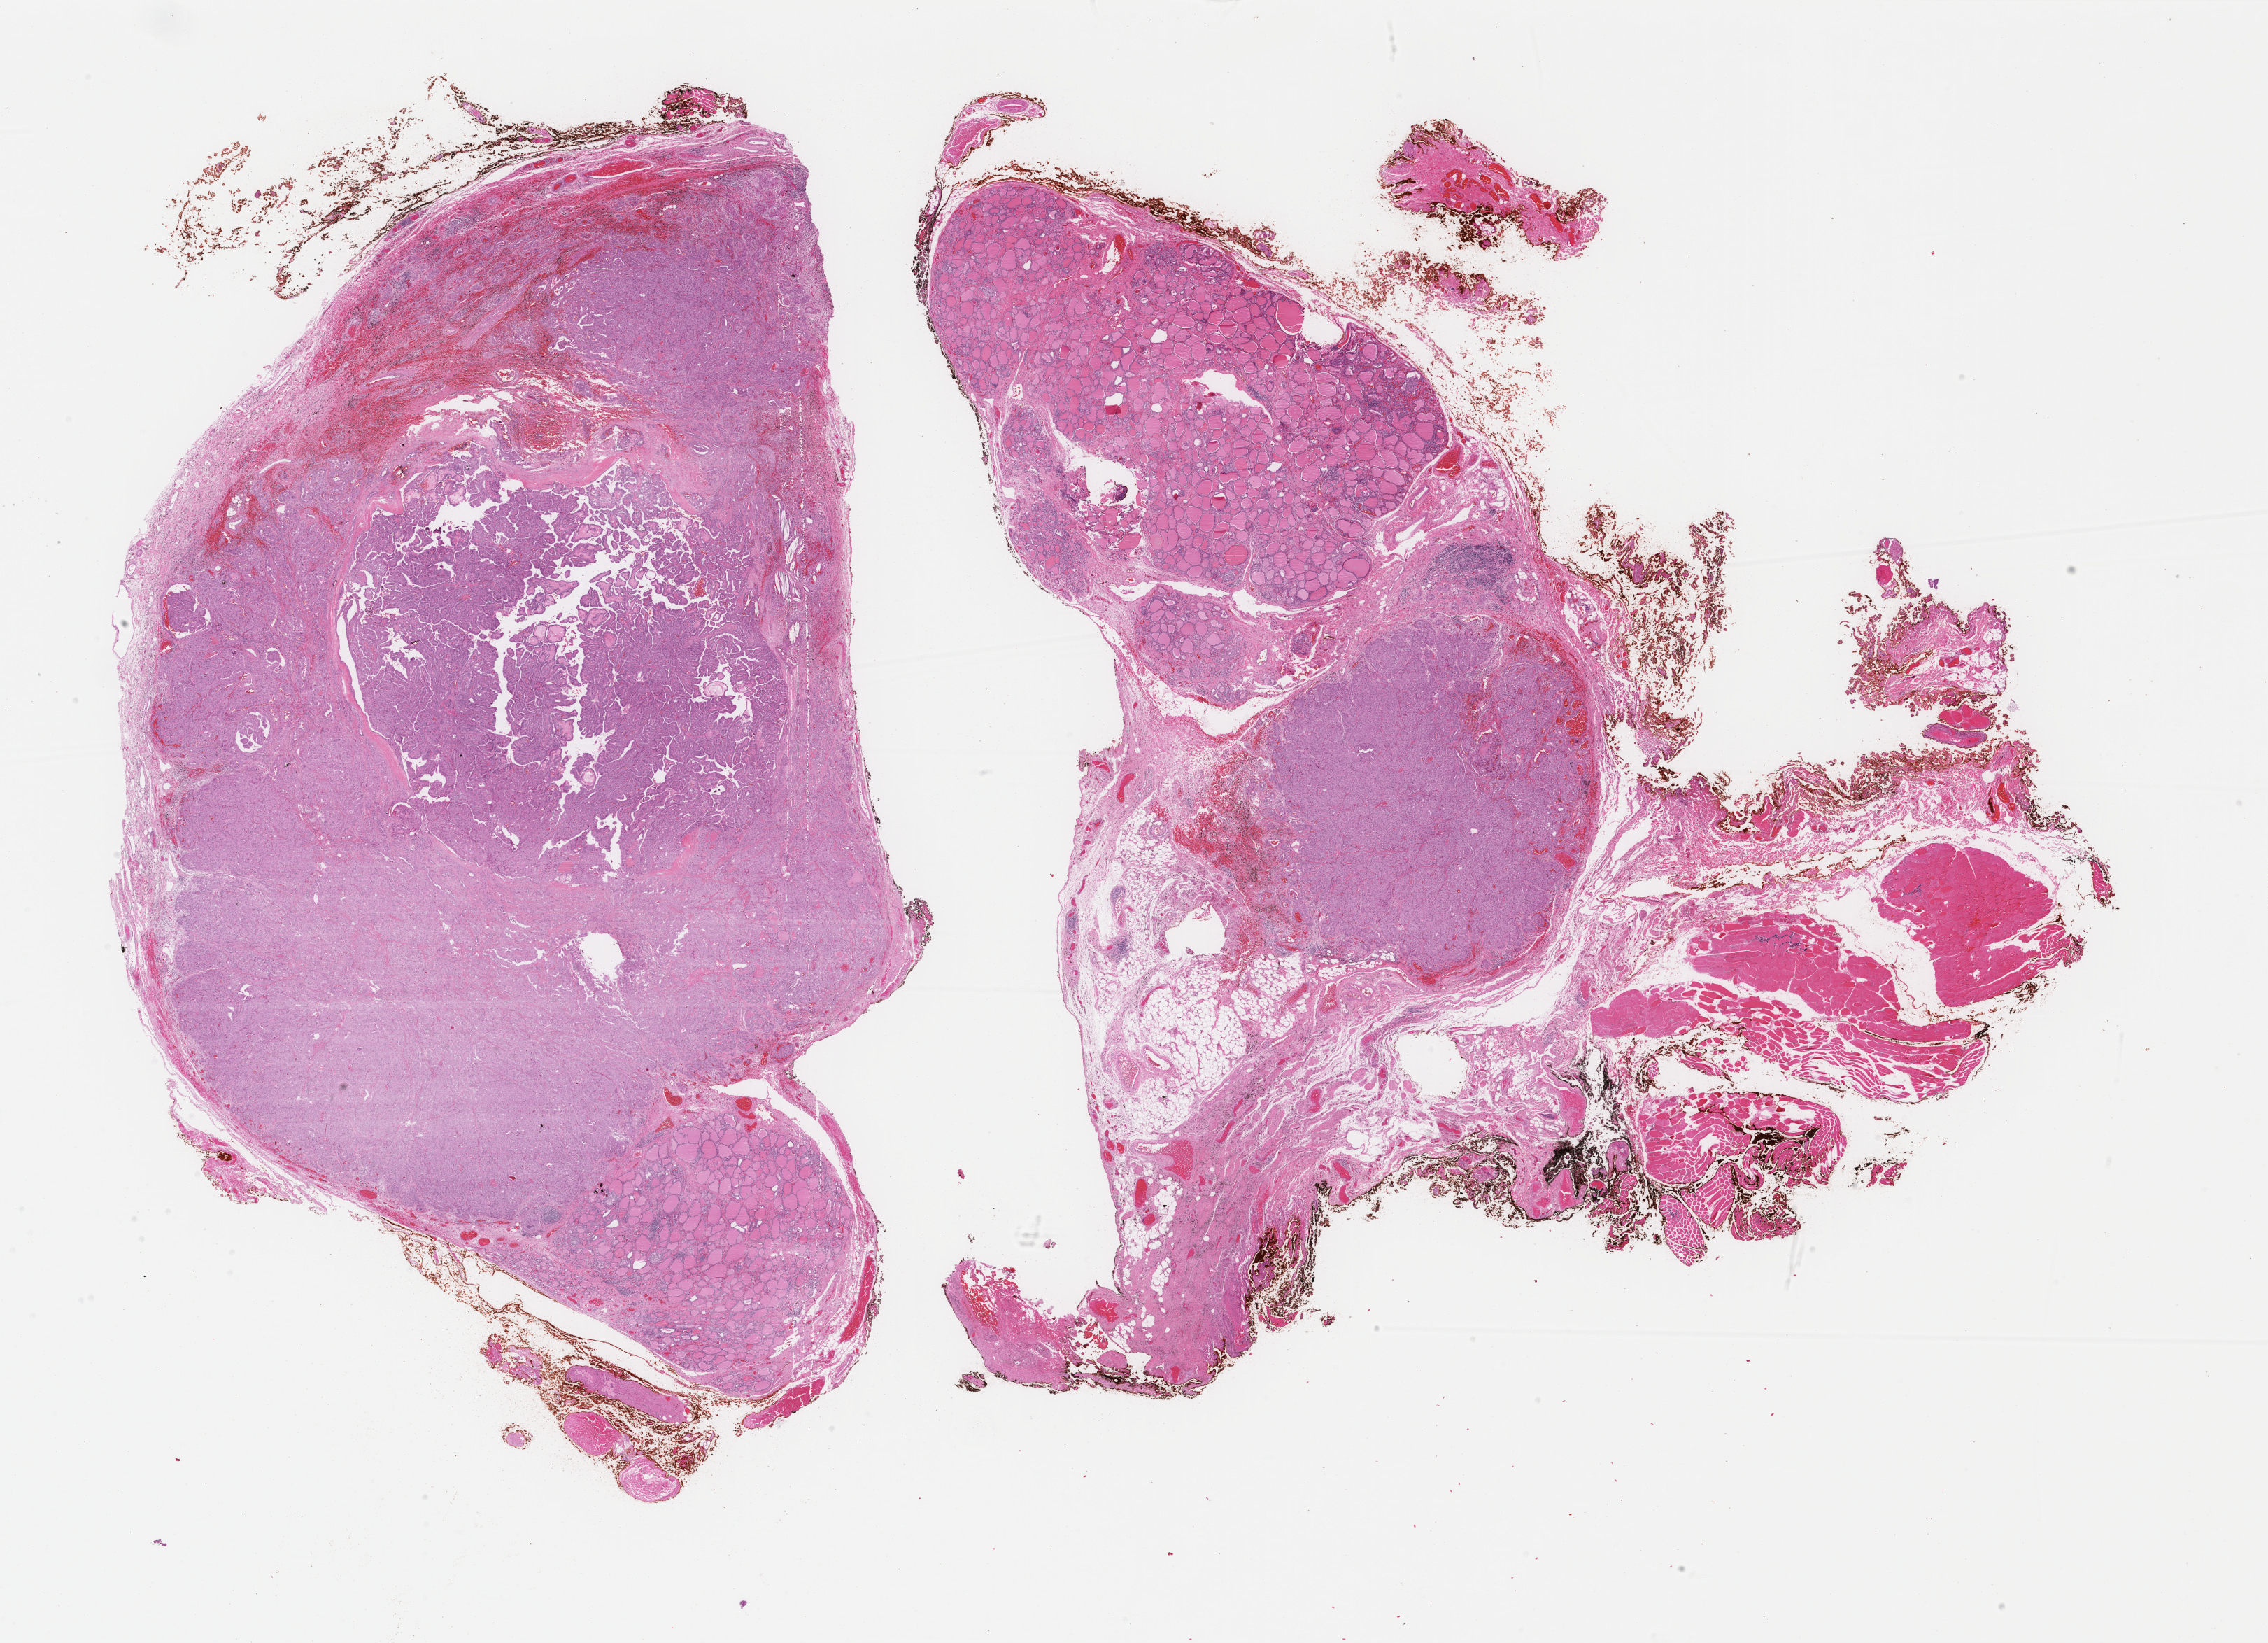
Hematoxylin and eosin (H&E) stained whole-slide image — low-resolution overview of the scanned area, about 25.7 x 18.6 mm (from a 40x scan); formalin-fixed paraffin-embedded (FFPE) diagnostic section; thyroid, primary tumour sample. Patient: female, age at initial diagnosis 60 years.
Lymph nodes positive (case pathology): 2 of 7 examined. AJCC pathologic stage: IVA. Pathologic diagnosis: Papillary carcinoma, columnar cell. Laterality: midline.